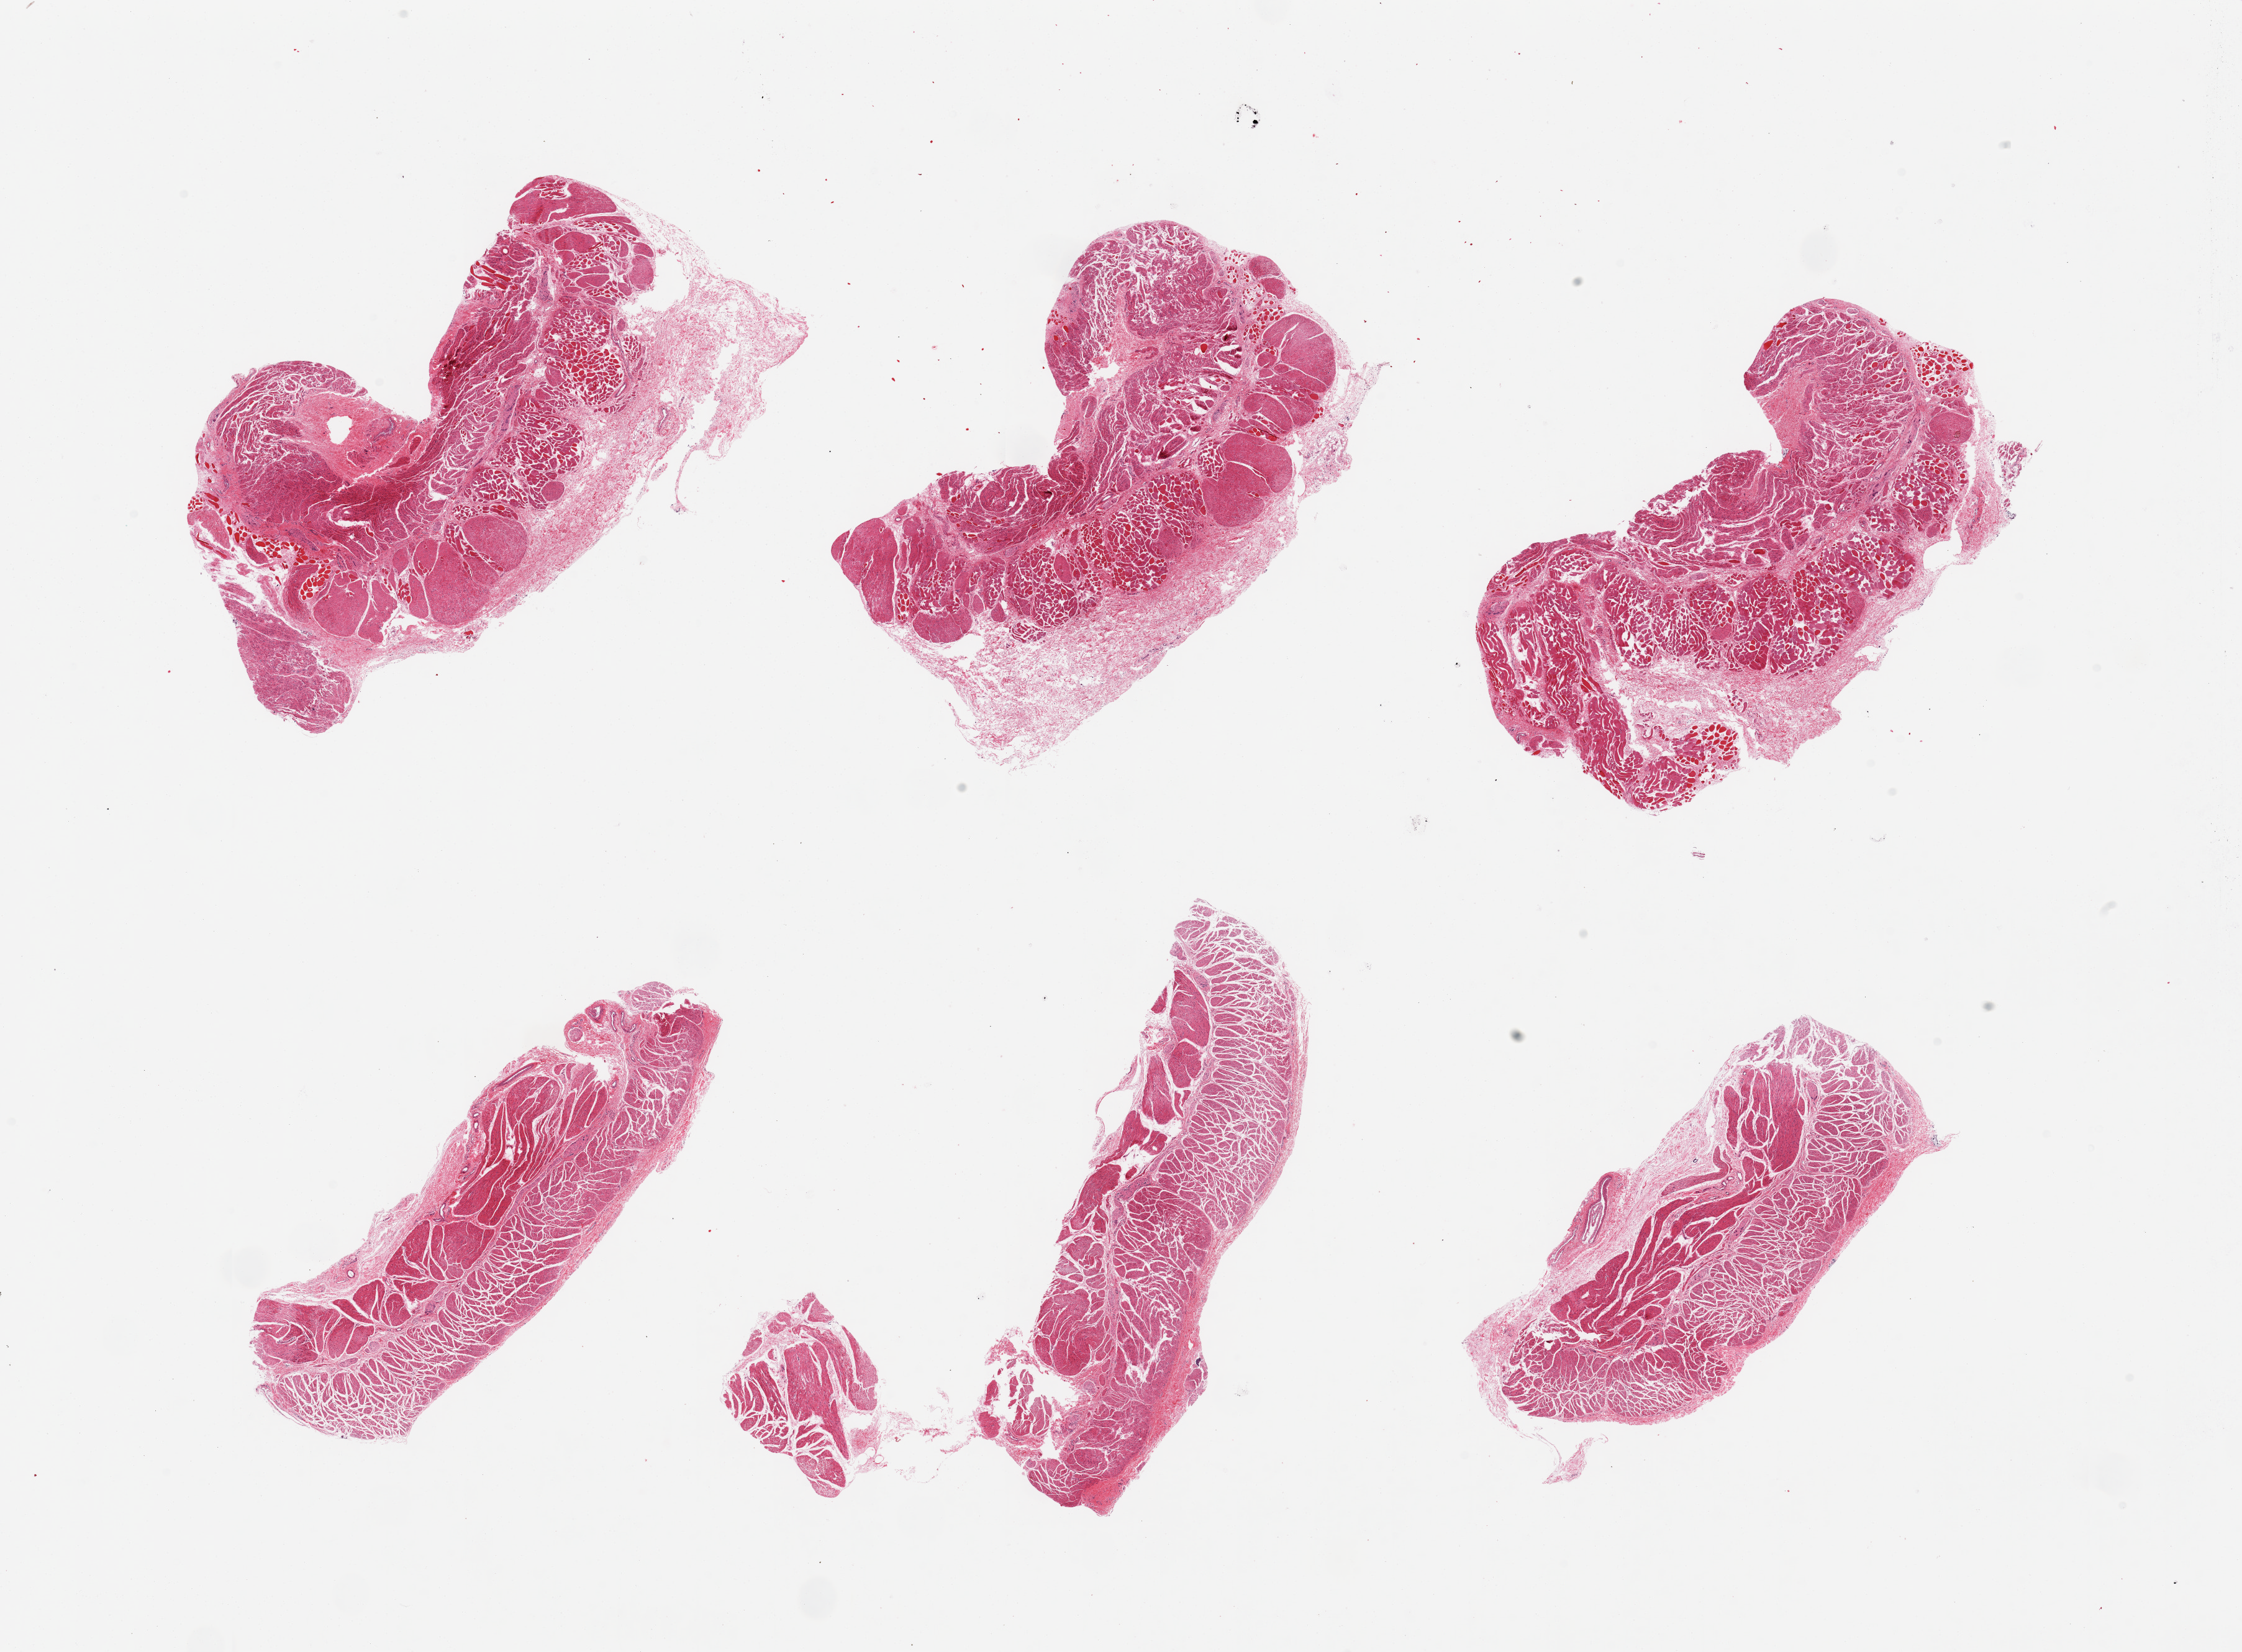
Digitized hematoxylin and eosin (H&E)-stained section, whole scanned area (about 28.5 x 21.0 mm, slide scanned at 20x) shown as a low-resolution overview.
• specimen: PAXgene-fixed, paraffin-embedded tissue; target tissue: esophageal muscle; donor tissue sample